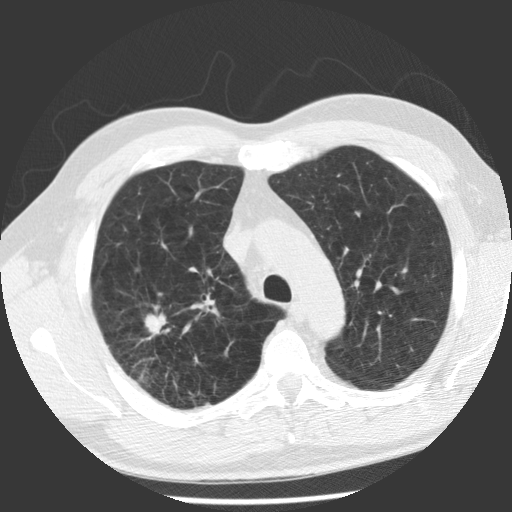
Low-dose screening chest CT, one axial slice. Slice 84 of 112 in the series (ordered by position). Reconstruction kernel STANDARD. 140 kVp. Lung window (W 1500 / L -600 HU). 2.5 mm slice thickness. 512 × 512 image matrix, field of view 344 × 344 mm.
Annotated regions visible in this slice (outlined manually by an expert reader):
- lesion 1 (tumor, upper lobe of right lung): bounding box <145,314,167,334> (left, top, right, bottom; pixels)